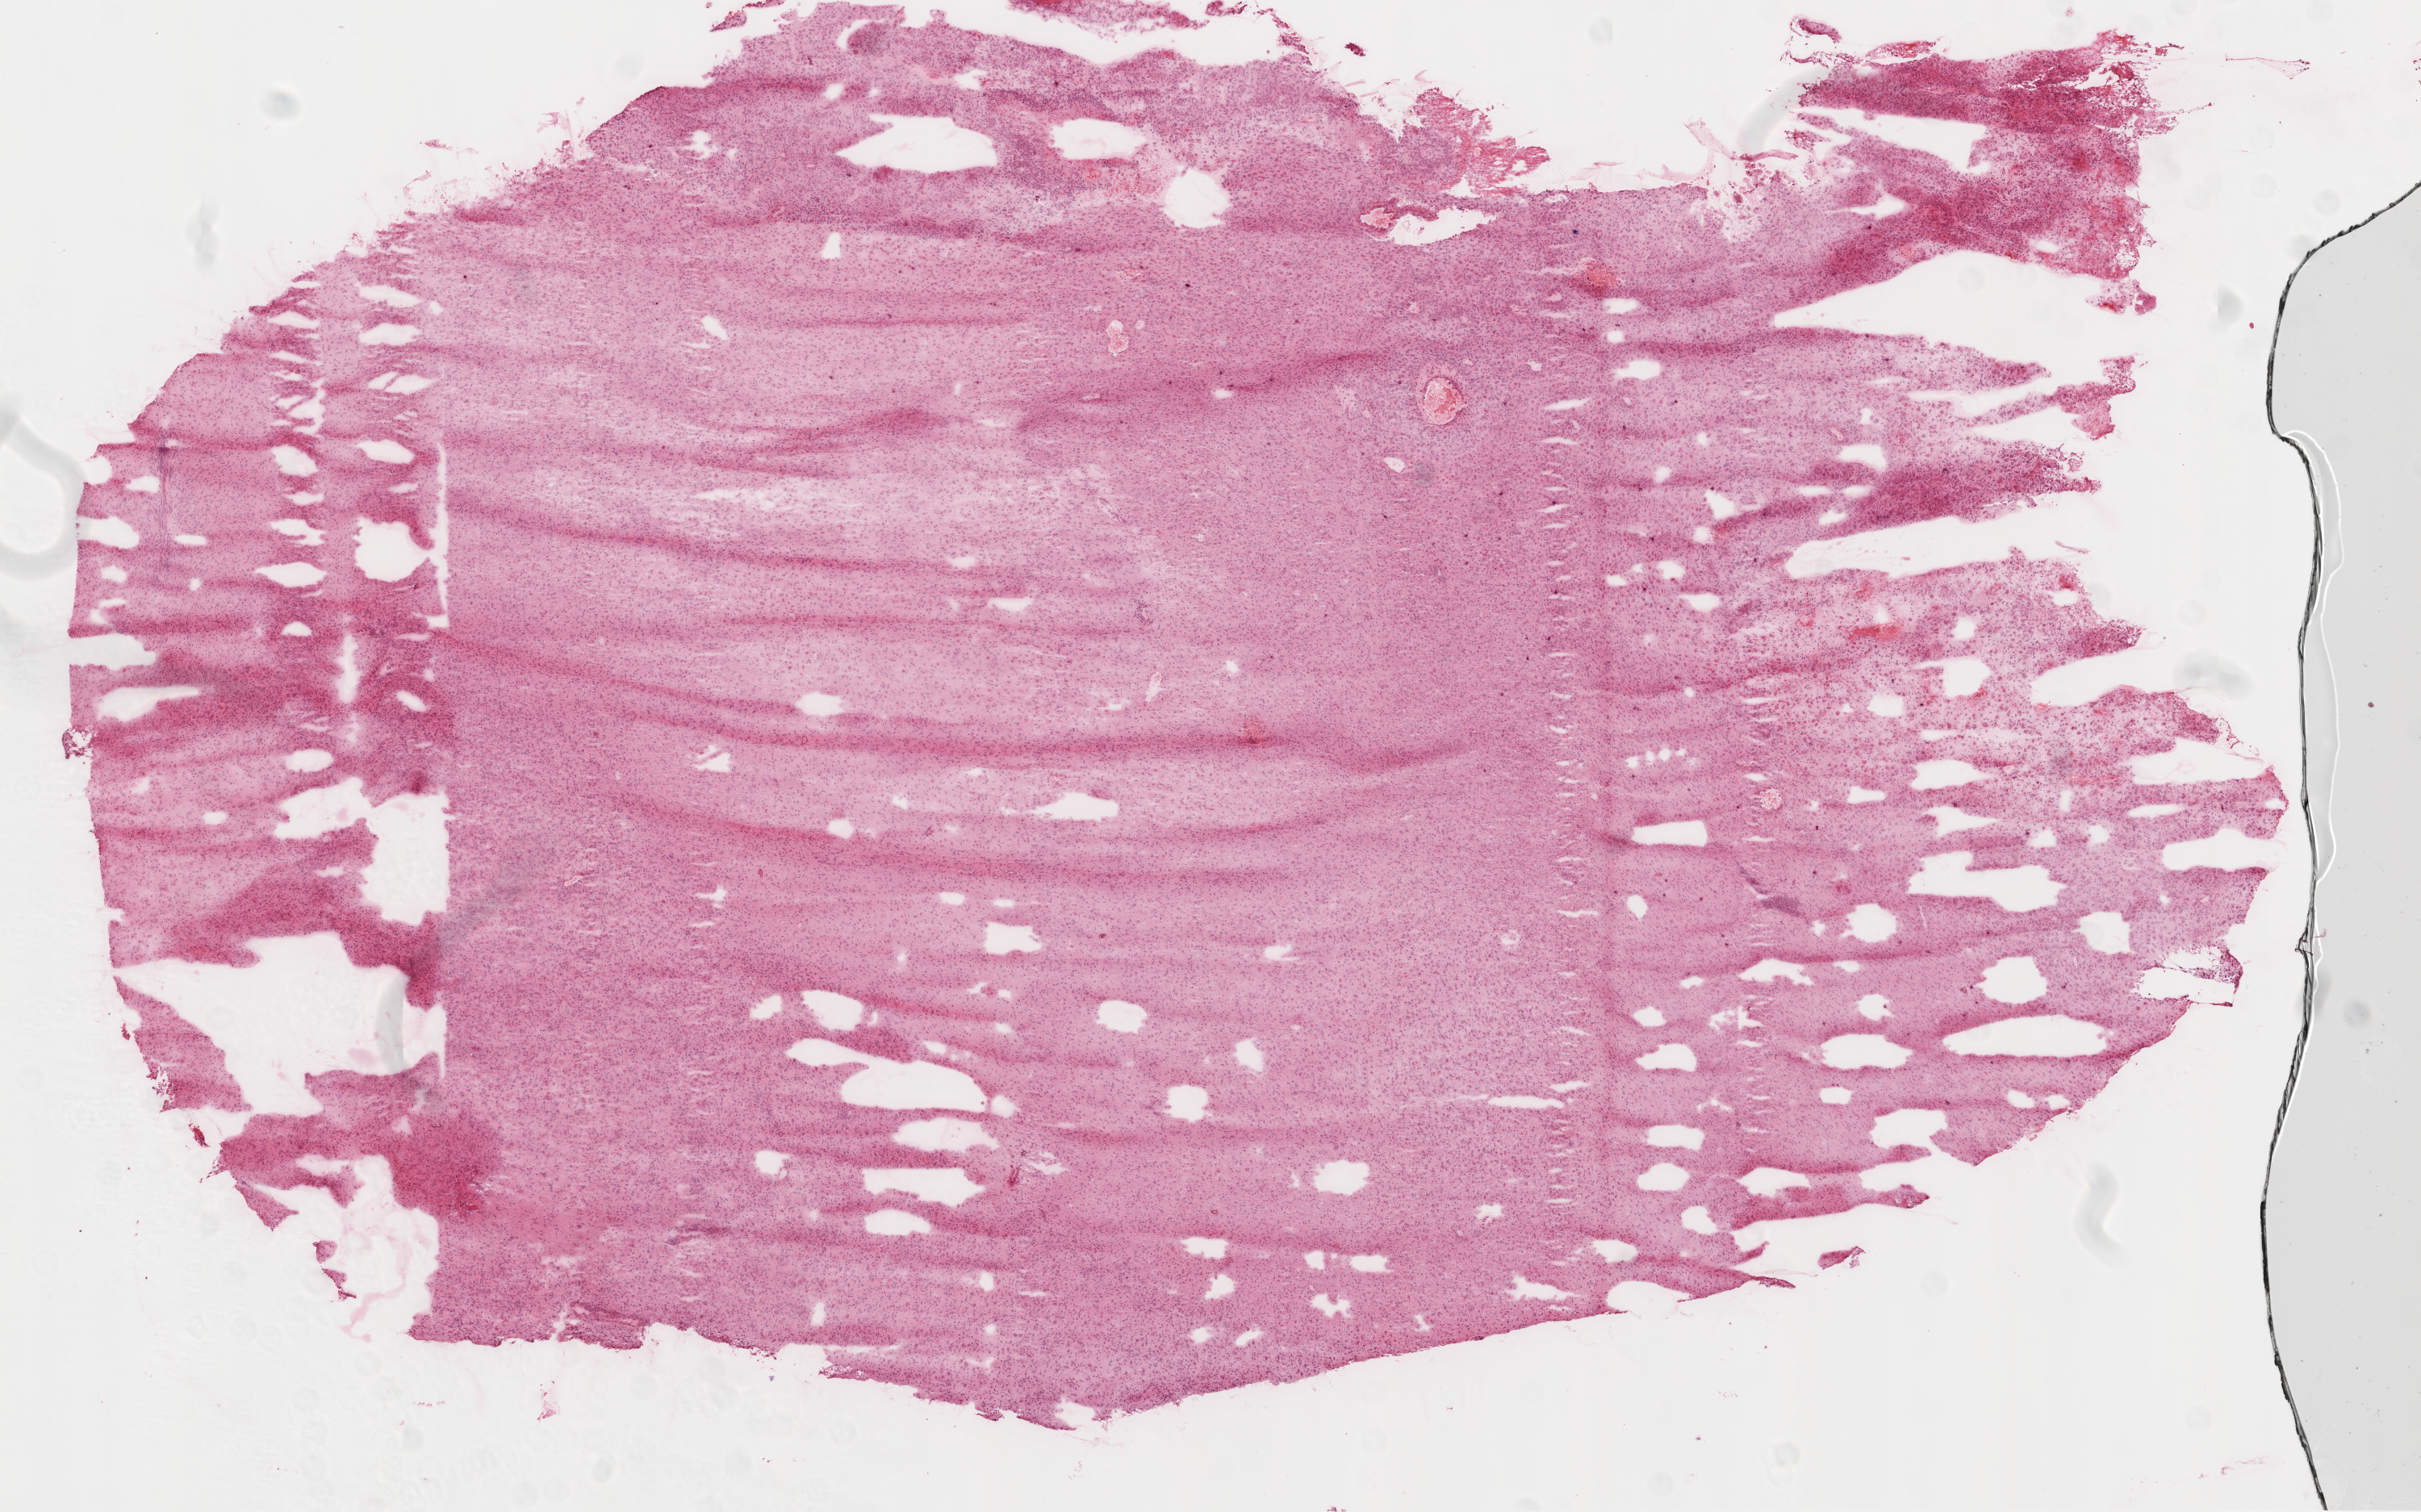
H&E-stained whole-slide image, low-resolution overview of the scanned area, about 12.0 x 7.5 mm (slide scanned at 20x), frozen section, sample: primary tumour, brain. Female patient; age at initial diagnosis 47 years. Slide review estimates, as recorded: tumour cells 80%, tumour nuclei 80%, normal cells 10%, stromal cells 5%, necrosis 5%.
• diagnosis: Glioblastoma